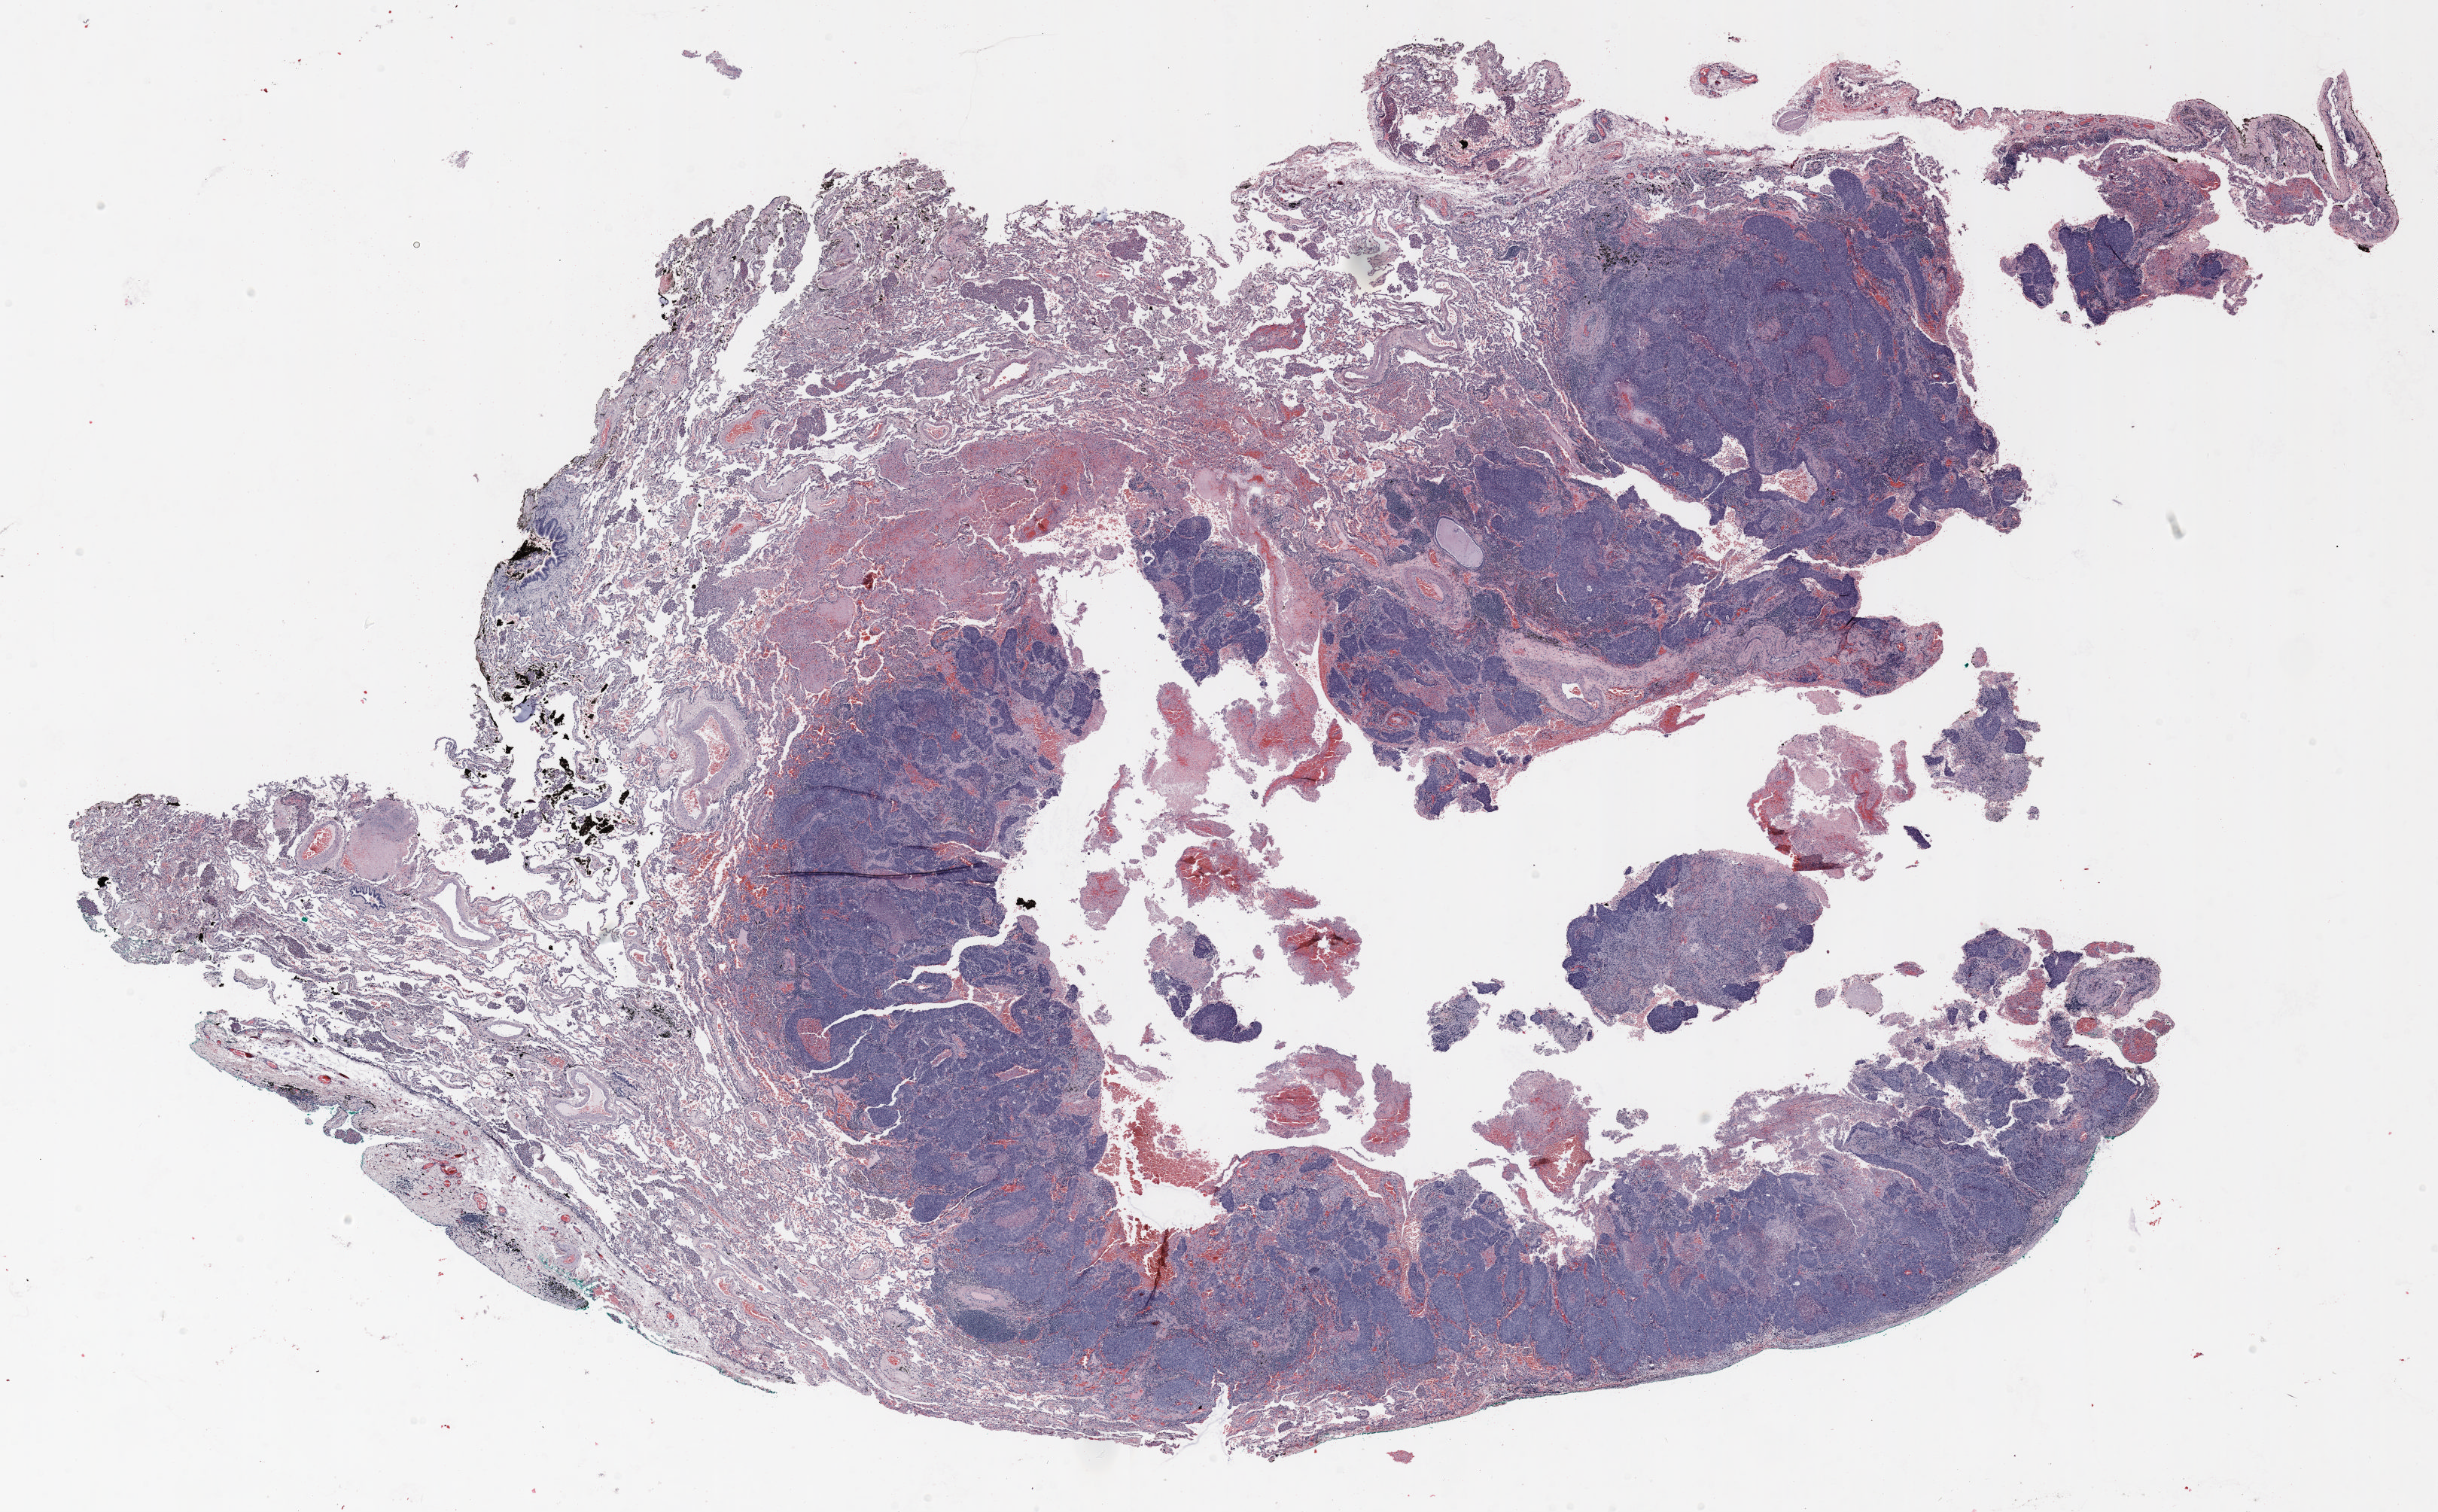
H&E whole-slide image, low-resolution overview of the scanned area, about 26.0 x 16.1 mm (acquisition: 20x scan). FFPE section. Lung. Male, age 58 at enrolment. Current smoker at enrolment. Grade: moderately differentiated (G2).
Primary tumour location (clinical record): right middle lobe. Stage (AJCC 6th edition): IA. ICD-O-3 topography: middle lobe of lung (C34.2). Tumour size (pathology): 24 mm. Participant's lung-cancer diagnosis: Squamous cell carcinoma, NOS (ICD-O-3 8070/3).